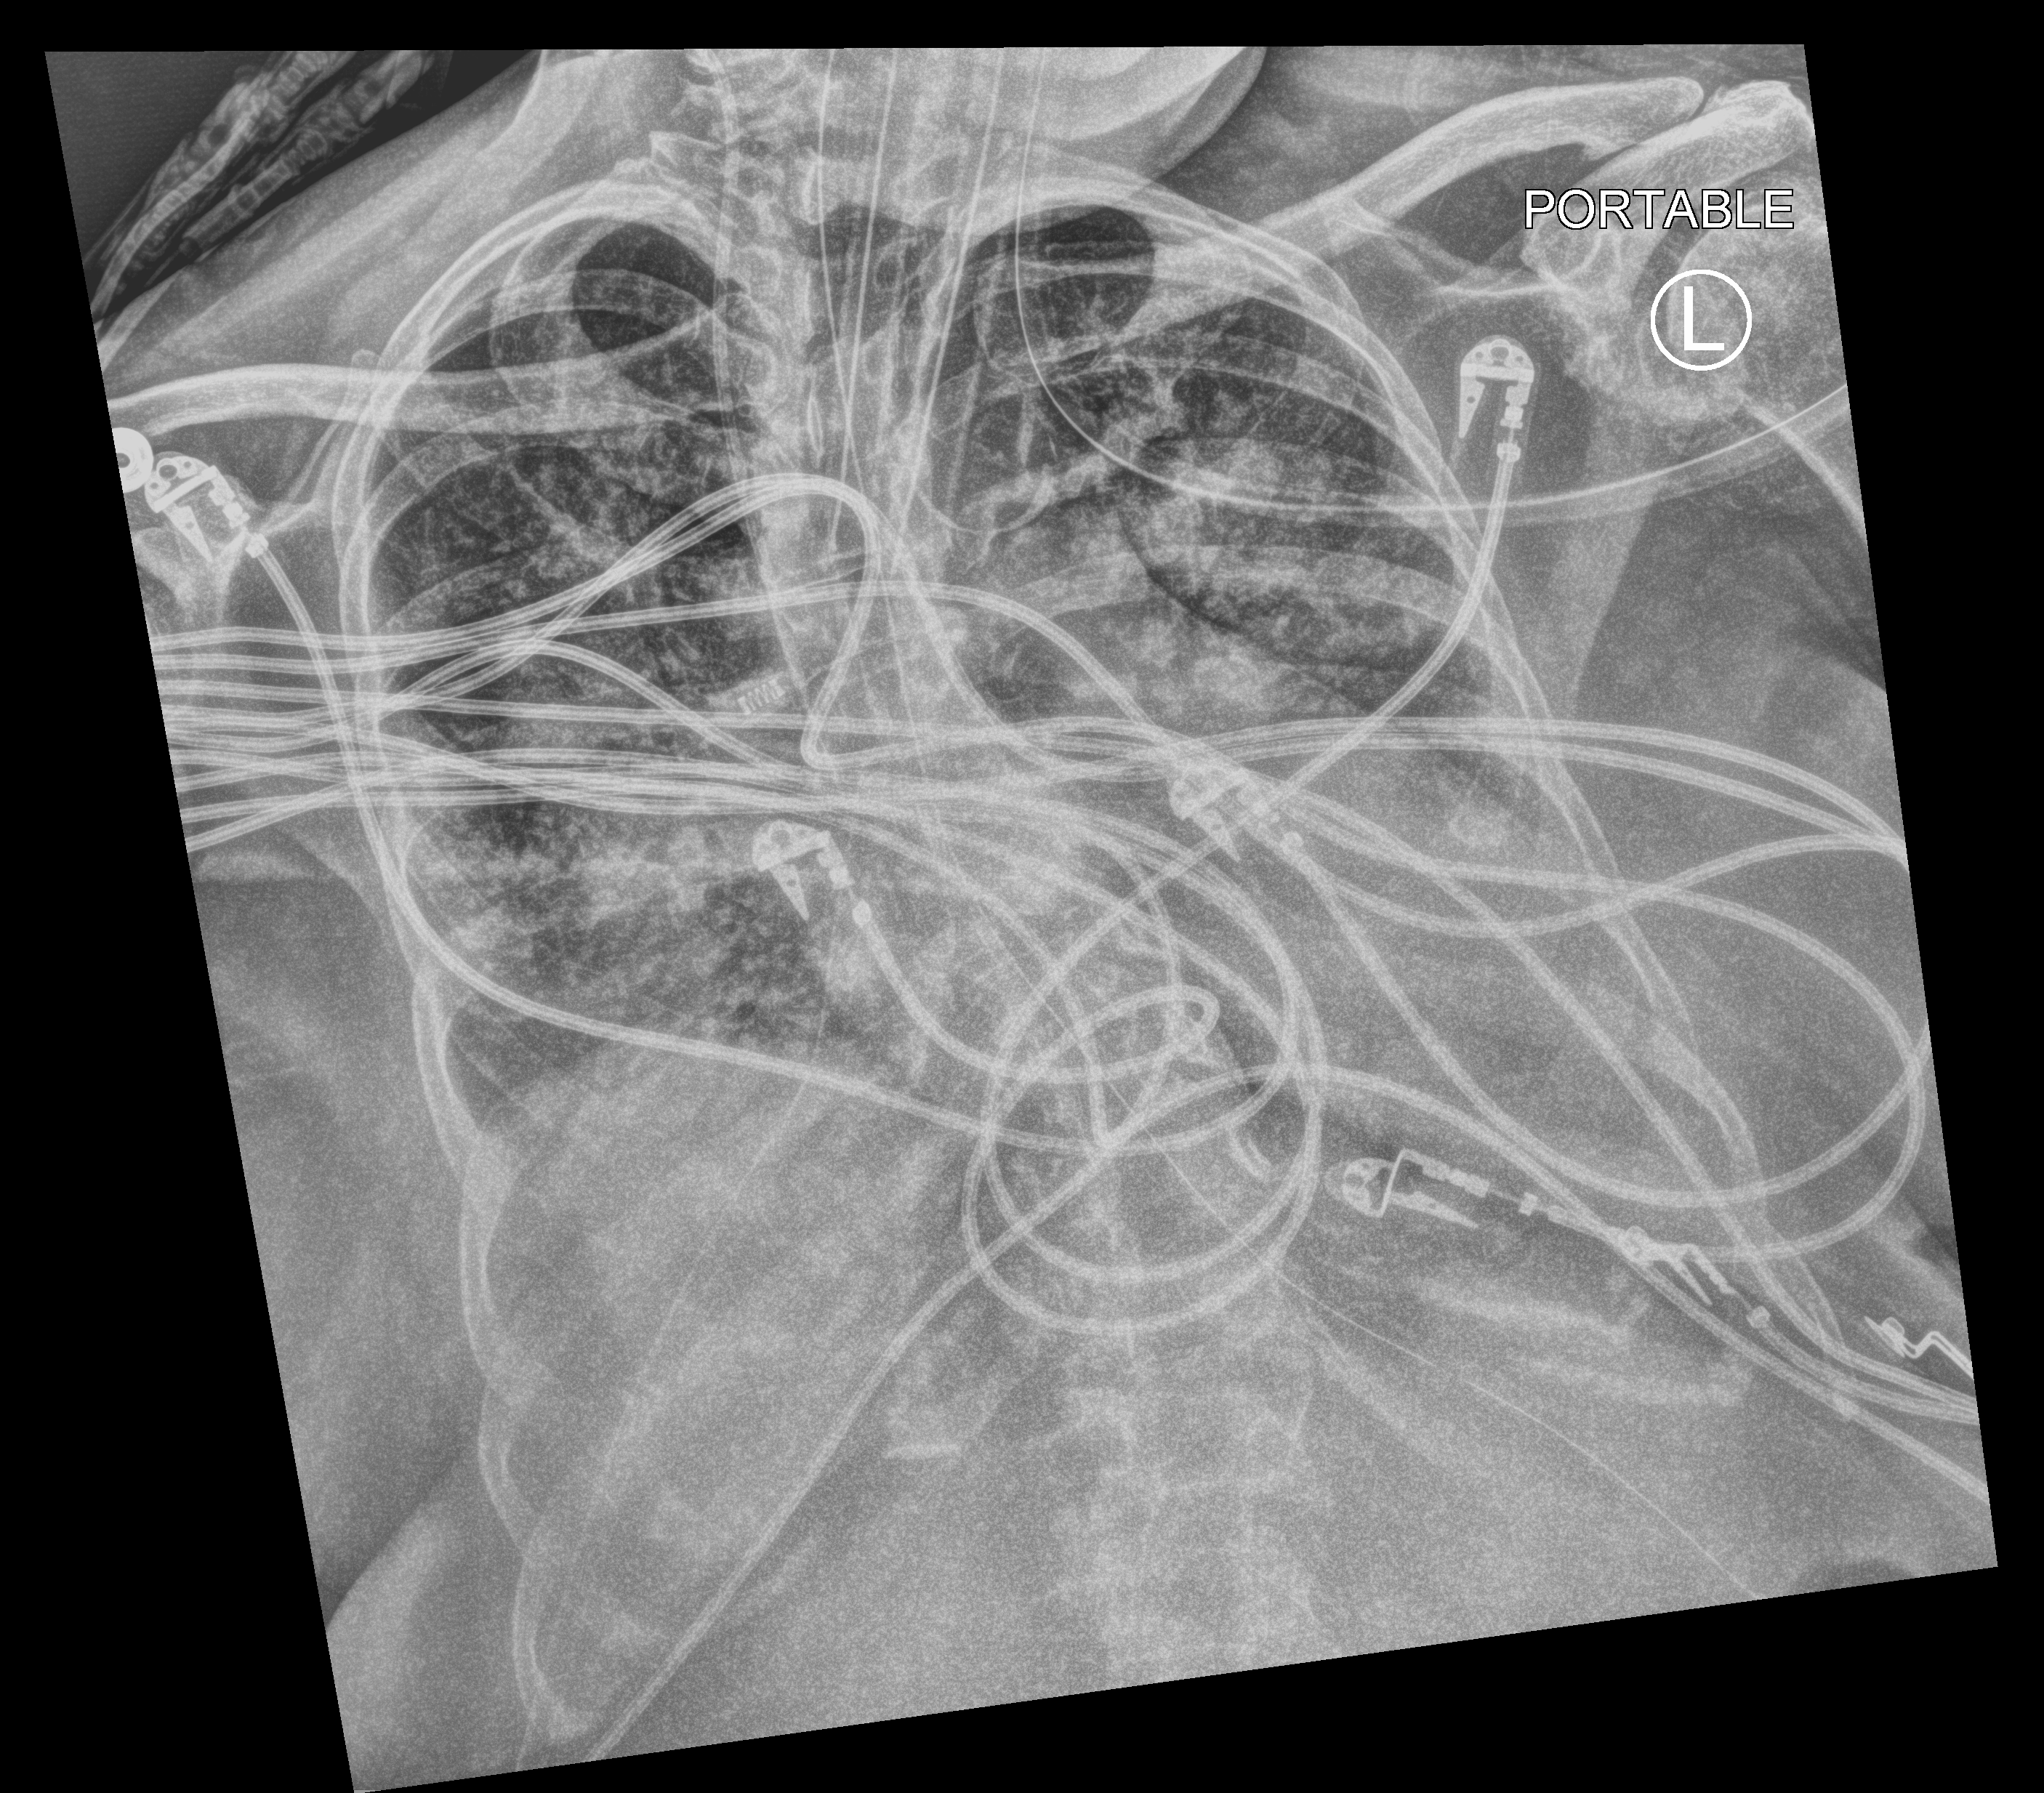
Chest X-ray (portable). Patient hospitalised with COVID-19; female, aged 60–74 years.
From the hospital-stay record, not from the radiograph (when in the stay this image was taken is not recorded): admitted to intensive care during this hospital stay: yes; mechanically ventilated during this hospital stay: yes.